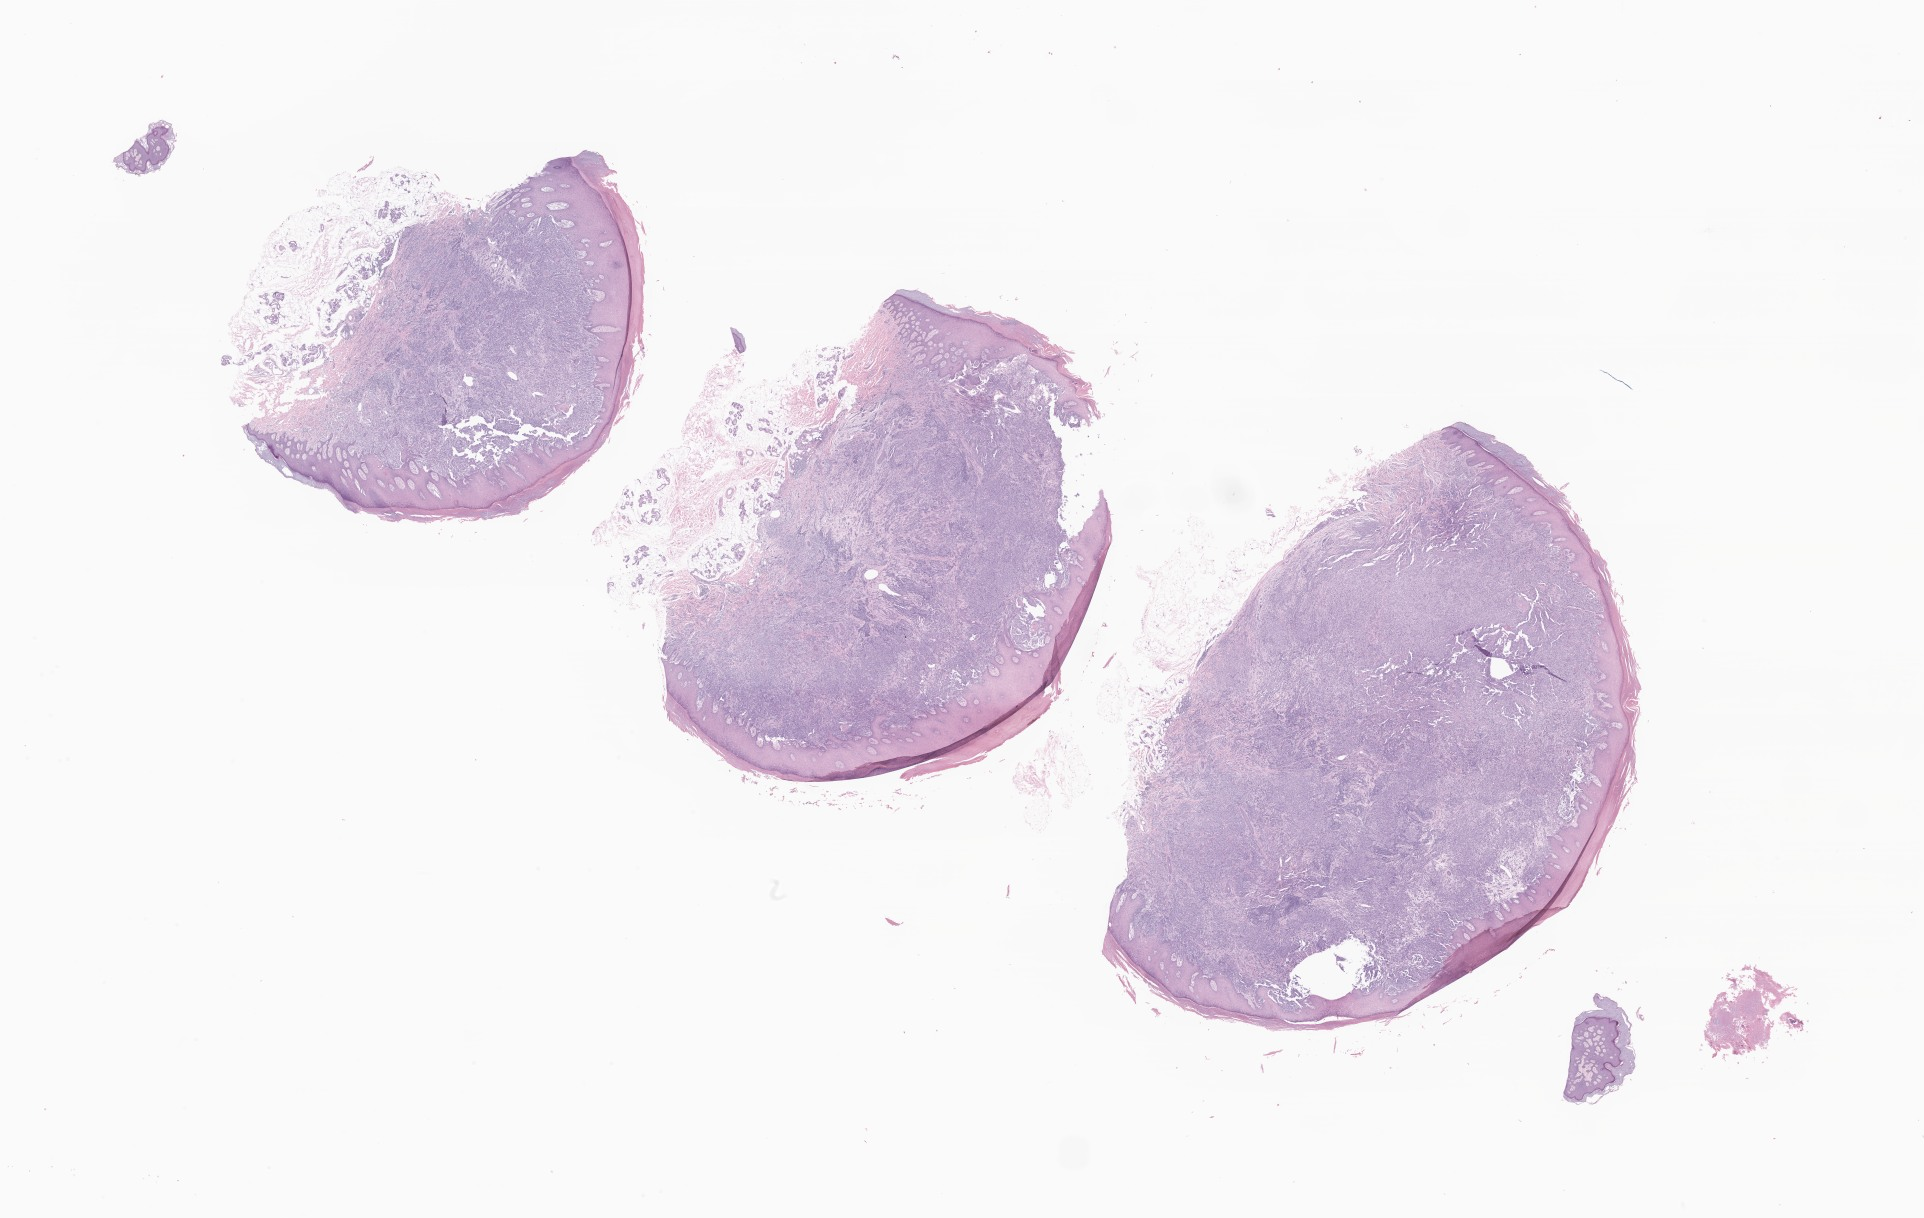
H&E whole-slide image of tumor tissue from the soft tissue — low-resolution overview of the scanned area, about 32.5 x 20.5 mm, FFPE section. Patient: female, age 247 months (20 years 7 months).
• diagnosis: Clear cell sarcoma, NOS